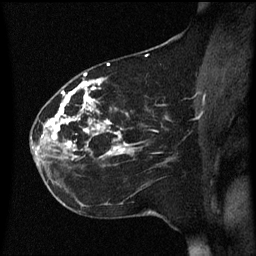
Breast MRI (dynamic contrast-enhanced), one sagittal slice; position 27 of 60 along the scan axis; dynamic contrast-enhanced series, image 2 of 3 at this slice position (ordered by acquisition); 1.5 T; TE 4.2 ms, TR 8.4 ms; 2.2 mm slice thickness; 256 × 256 image matrix. Patient: female, 35 years. Case-level facts recorded for this patient, not image findings: setting: breast cancer imaged before/during neoadjuvant chemotherapy; receptor status: HER2-positive.
Annotated regions visible in this slice (semi-automatic segmentation, software-assisted and operator-edited):
- analysis volume of interest (the breast-tissue region the enhancement analysis was run in; not a lesion): bounding box <32,78,173,163> (left, top, right, bottom; pixels)
- tumour enhancement mask (voxels above the 70 % enhancement threshold inside the analysis volume of interest): <38,78,134,157>